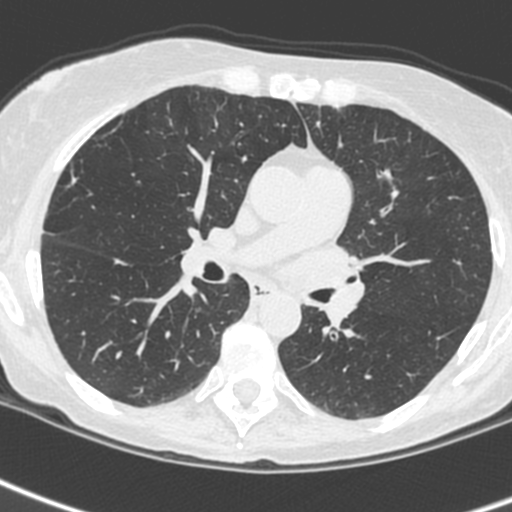
Low-dose screening chest CT, one axial slice; position 139 of 242 along the scan axis; lung window (W 1500 / L -600 HU); 1.3 mm slice thickness; 512 × 512 image matrix.
Annotated regions visible in this slice (expert manual segmentation):
- lesion 3 (tumor, upper lobe of left lung): bounding box <293,243,365,322> (left, top, right, bottom; pixels)